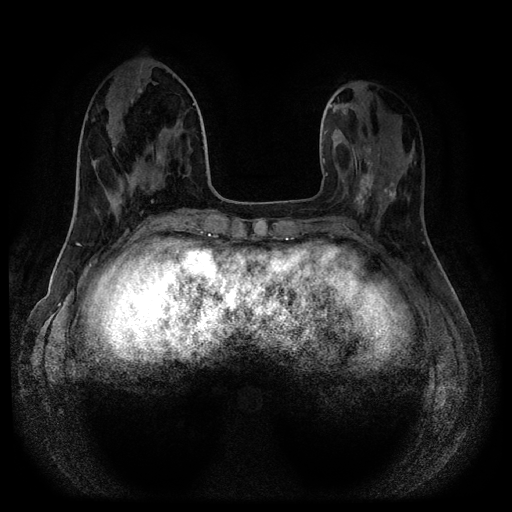
Breast MRI (dynamic contrast-enhanced, multi-phase), one axial slice; position 38 of 116 along the scan axis; dynamic contrast-enhanced series, time point 2 of 5 at this slice position (early post-contrast); 1.5 T; TE 2.7 ms, TR 5.4 ms; 2 mm slice thickness; 512 × 512 image matrix, field of view 340 × 340 mm. Patient: female, 40 years.
Structures marked on this image (semi-automatically segmented with operator editing):
- breast lesion (labelled benign in the annotation): box from (x=351, y=146) to (x=381, y=218) px